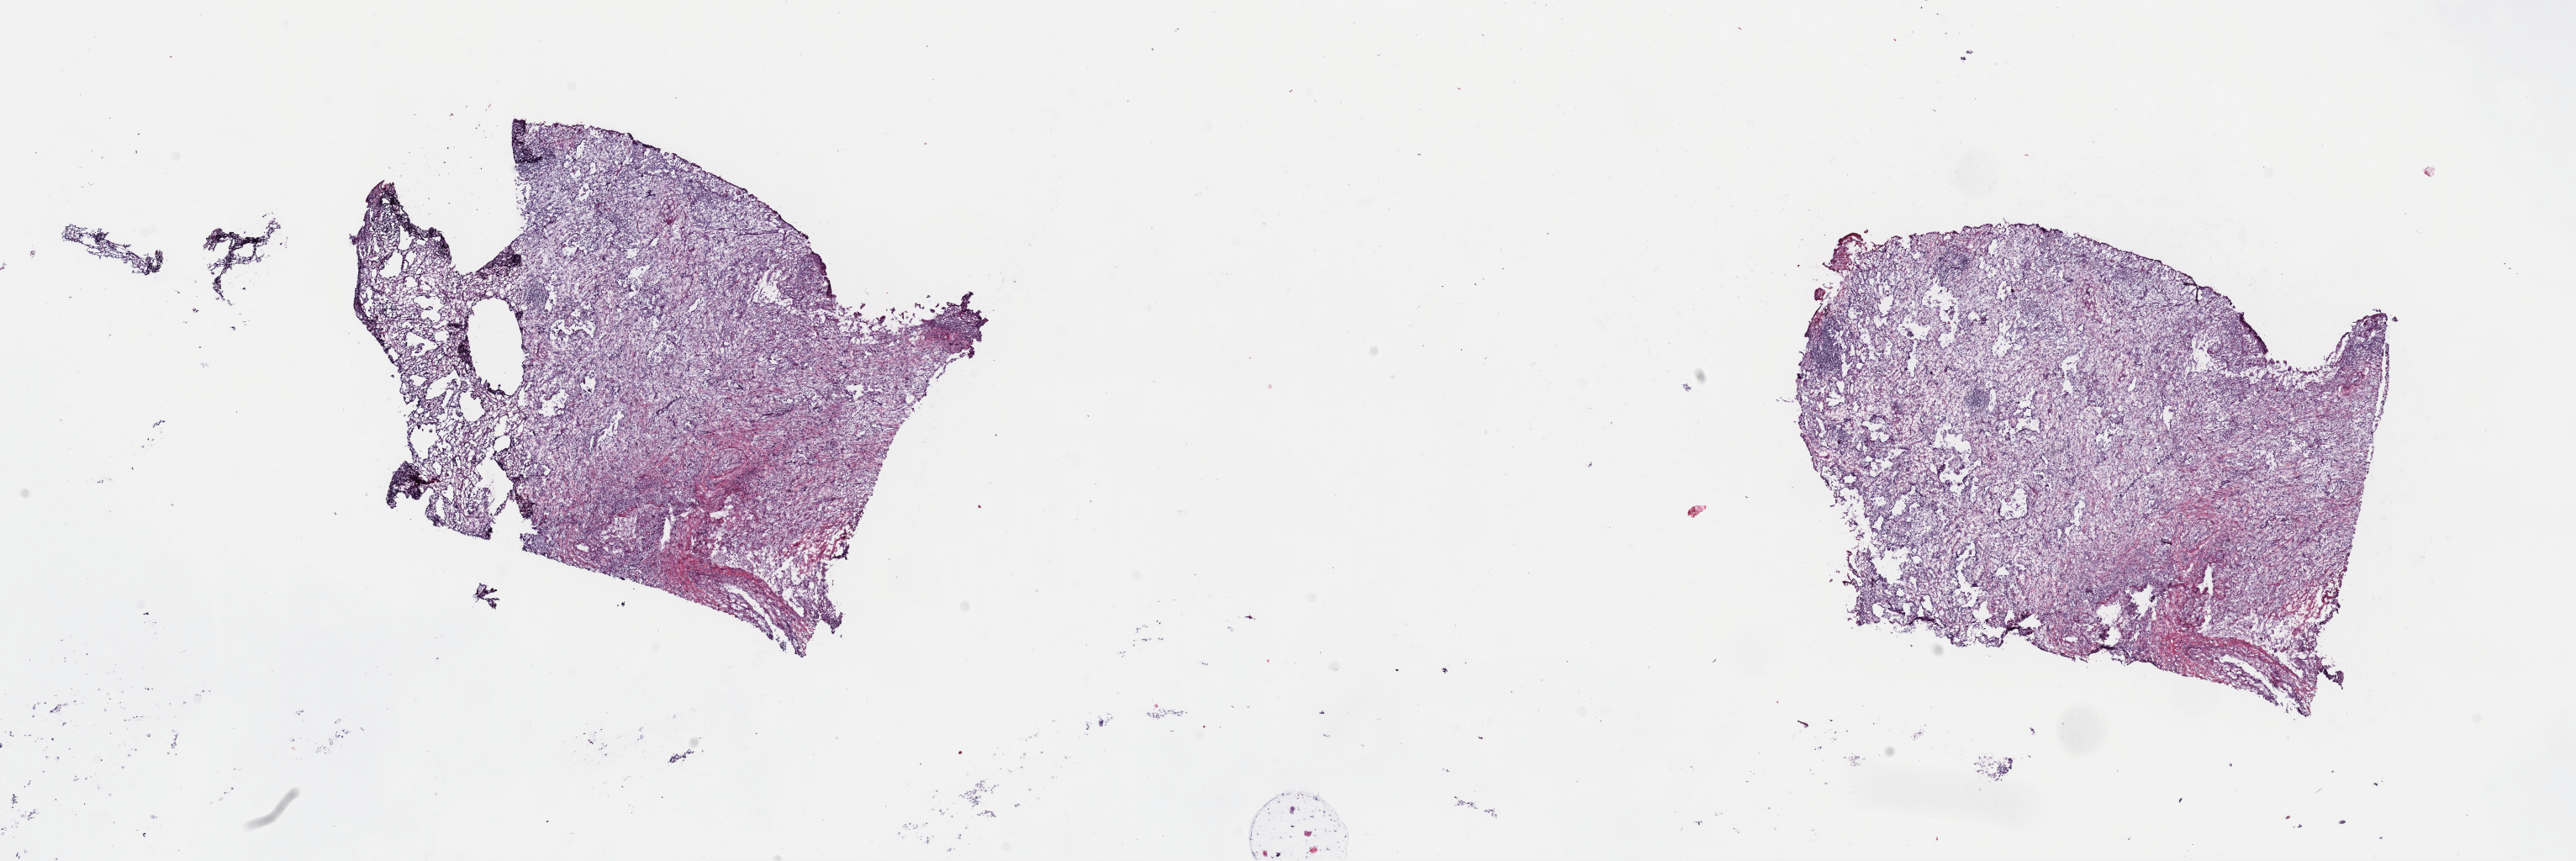
H&E-stained whole-slide image — whole scanned area (about 24.2 x 8.1 mm, slide scanned at 40x) shown as a low-resolution overview; frozen section from the top of the tissue portion; primary tumour sample from the lung. Male, age 68 years at initial diagnosis. Slide review estimates, as recorded: tumour cells 70%, tumour nuclei 70%, normal cells 0%, stromal cells 30%, necrosis 0%. Infiltration values recorded for this section: lymphocyte infiltration 4%, monocyte infiltration 2%, neutrophil infiltration 3%.
* AJCC pathologic stage: IIB (7th edition)
* laterality: right
* pathologic diagnosis: Squamous cell carcinoma, keratinizing, NOS (upper lobe, lung)
* TNM: T3 N0 M0